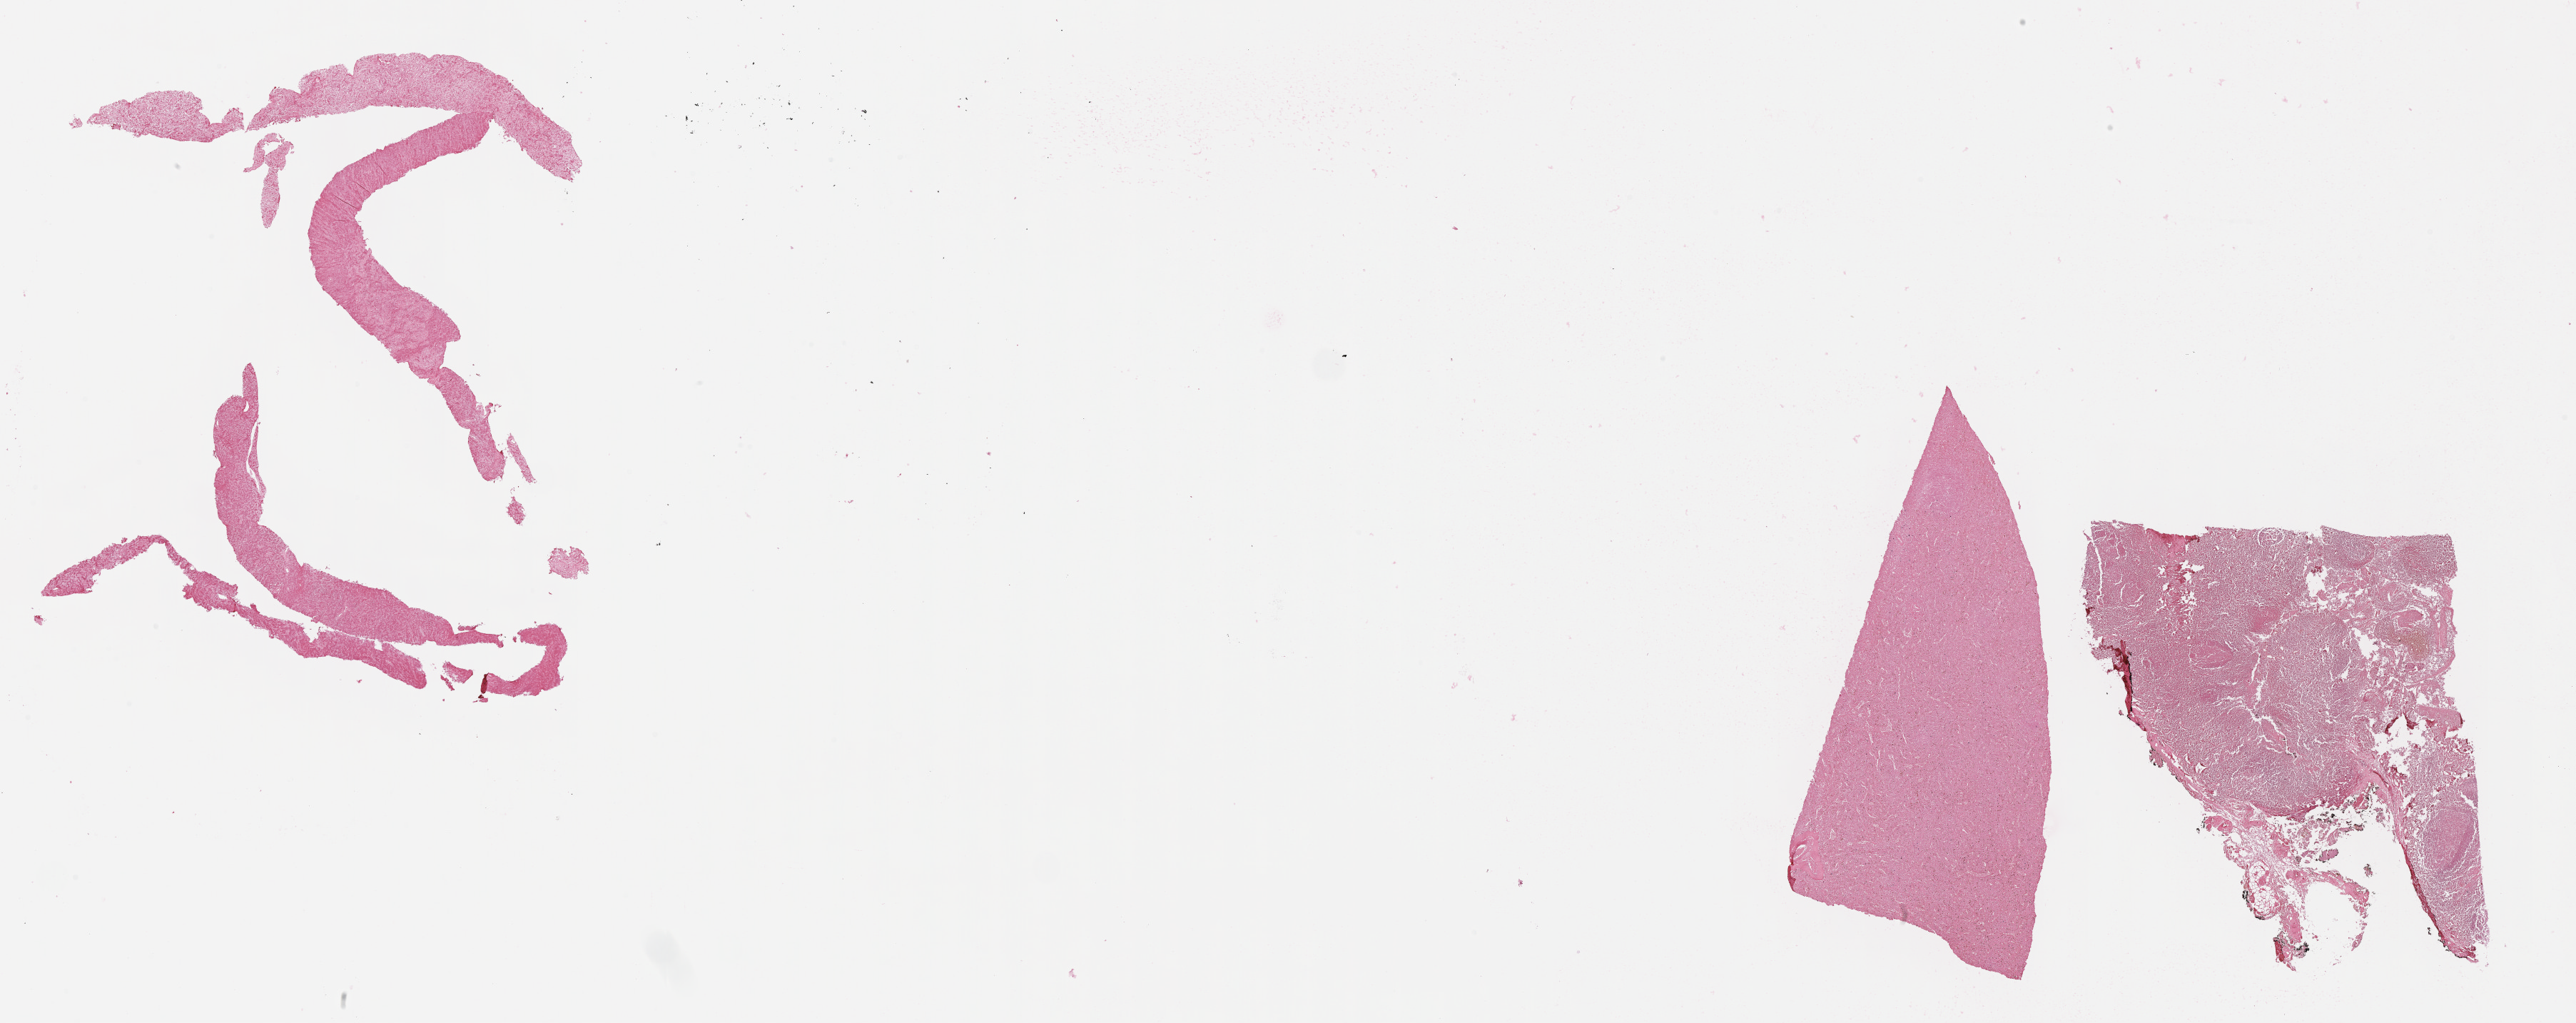
In-situ hybridisation whole-slide image, Epstein–Barr virus-encoded RNA (EBER) probe — shown as a low-resolution overview of the whole scanned area (about 29.2 x 11.6 mm). Specimen: tumor tissue. Site: pleura. Patient: male, age at initial diagnosis 2 years.
* histologic diagnosis: Diffuse large B-cell lymphoma, NOS